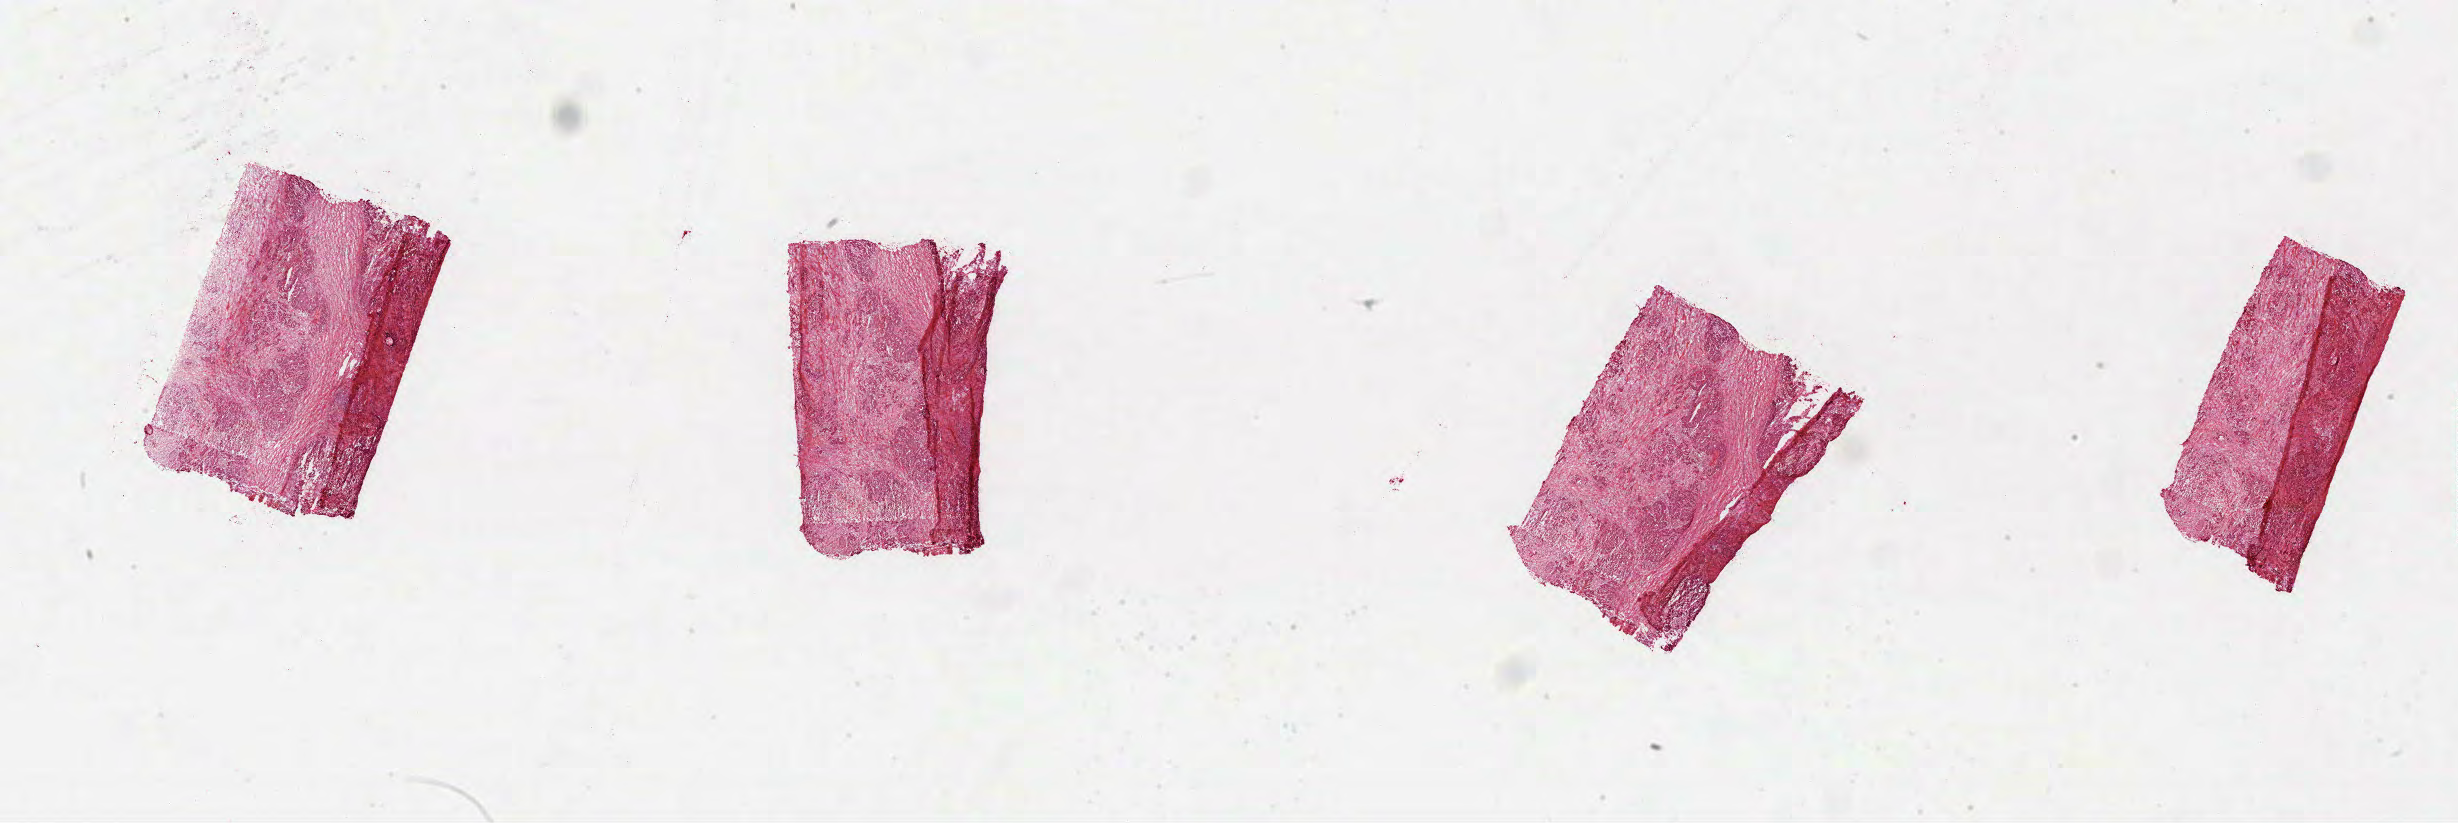
Whole-slide histology image, H&E-stained — whole scanned area (about 39.6 x 13.3 mm, from a 40x scan) shown as a low-resolution overview. Frozen section. Sample: primary tumour, rectum. Patient: male, age at initial diagnosis 33 years. Composition of this section per pathologist review: tumour cells 40%, tumour nuclei 60%.
Pathologic diagnosis: Adenocarcinoma with mixed subtypes.